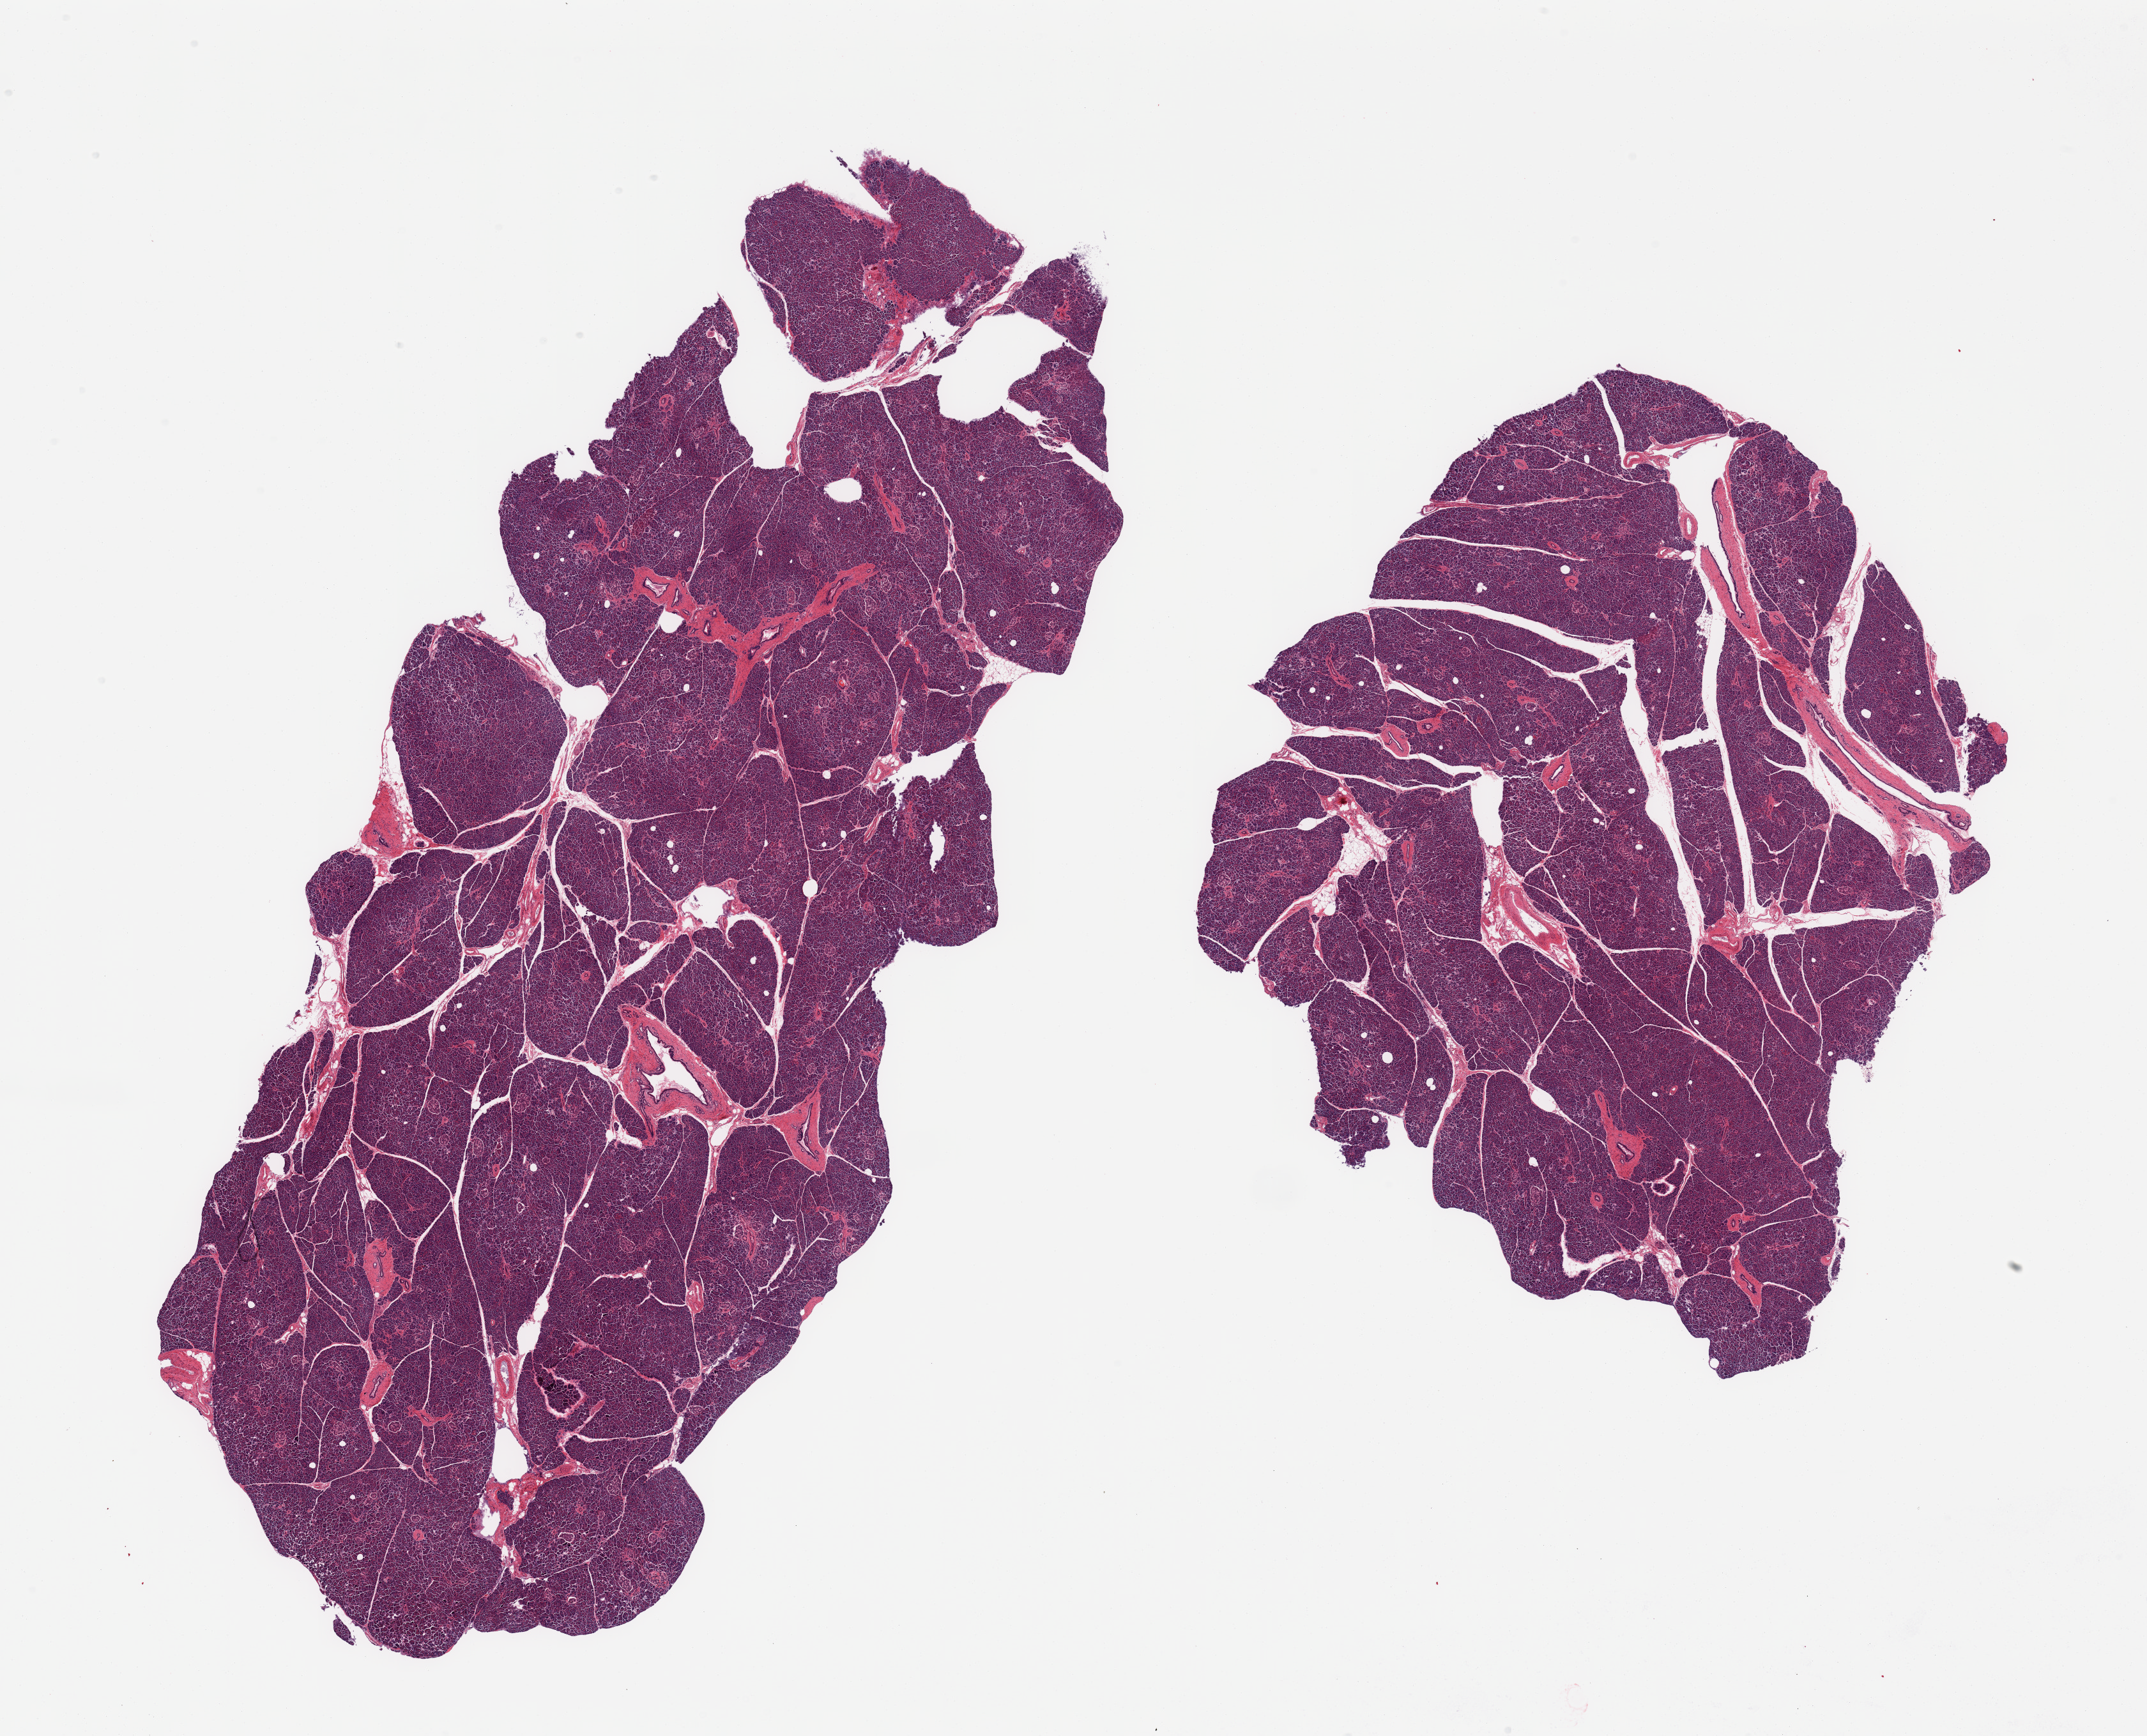
Hematoxylin and eosin (H&E) whole-slide image, low-resolution overview of the scanned area, about 26.6 x 21.5 mm (acquisition: 20x scan). PAXgene-fixed paraffin-embedded (PFPE) section. Section of pancreas (target tissue). Tissue donor sample.
- reviewer comment on this tissue sample: 2 pieces; ~10 % internal fat; accentuation of periductal fibrosis; Langerhans islets present